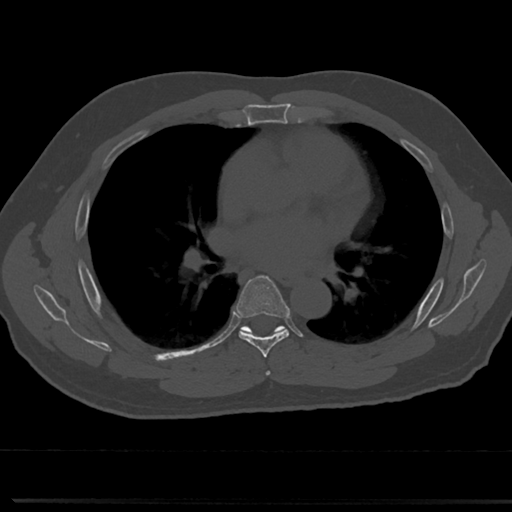
CT including the spine, one axial slice; position 442 of 817 along the scan axis; reconstruction kernel Br40s/3; bone window (W 1800 / L 400 HU); 0.5 mm slice thickness; 512 × 512 image matrix, field of view 355 × 355 mm. Male patient, age 61 years. From the clinical record (not read from this slice): primary cancer: prostate.
Outlined on this slice (semi-automatically segmented with operator editing):
- T5 vertebra: bounding box (x1, y1, x2, y2) in pixels: (264, 357, 273, 377)
- T6 vertebra: (220, 277, 309, 353)